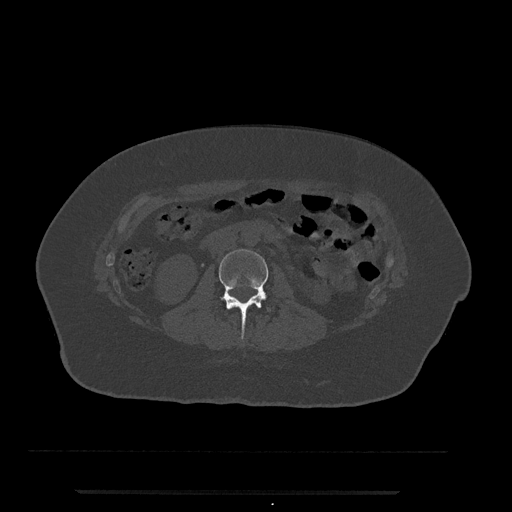
CT including the spine, one axial slice; position 33 of 797 along the scan axis; reconstruction kernel Br40s/3; 120 kVp; bone window (W 1800 / L 400 HU); 512 × 512 image matrix, field of view 440 × 440 mm. Patient: female, 51 years. Case-level facts recorded for this patient, not image findings: primary cancer: neuro; vertebrae with lytic lesions (as recorded): T8.
Outlined on this slice (semi-automatic segmentation, software-assisted and operator-edited):
- L2 vertebra: bounding box (x1, y1, x2, y2) in pixels: (219, 249, 269, 333)